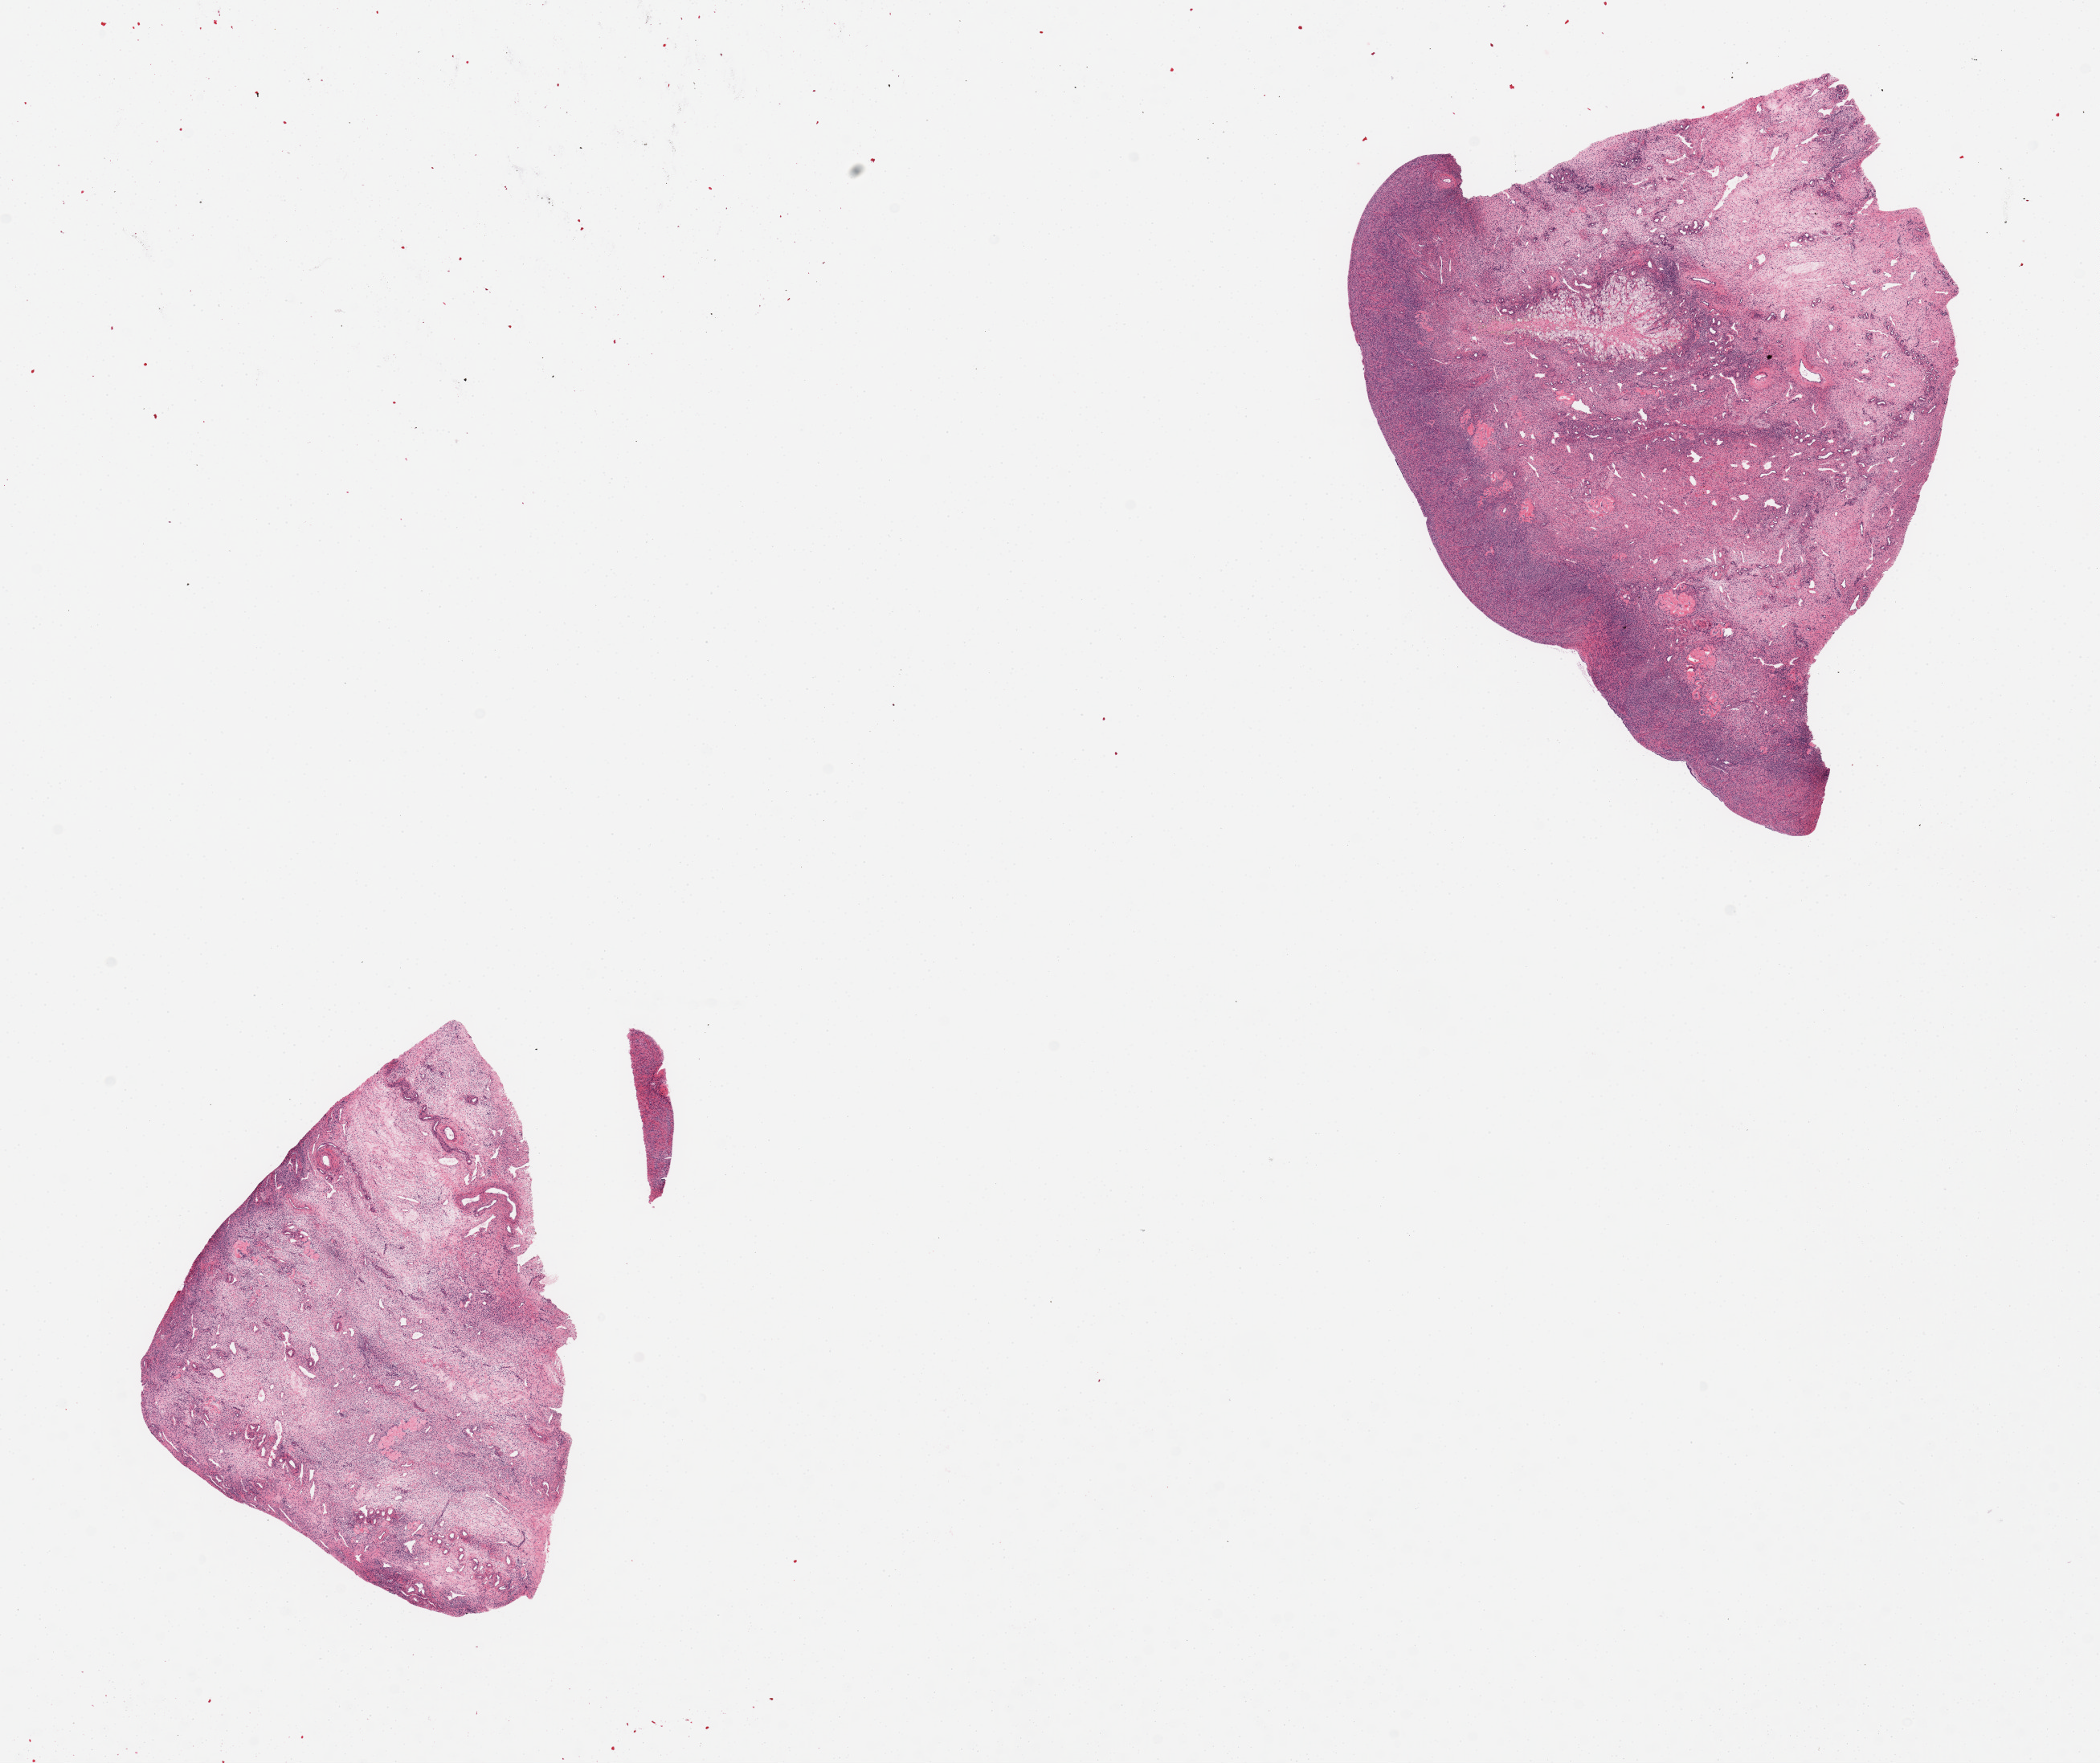
H&E whole-slide image, whole scanned area (about 20.7 x 17.4 mm, slide scanned at 20x) shown as a low-resolution overview; PAXgene-fixed, paraffin-embedded tissue; target tissue: ovary; donor tissue sample. Female donor.
Review note (as recorded): 2 pieces.